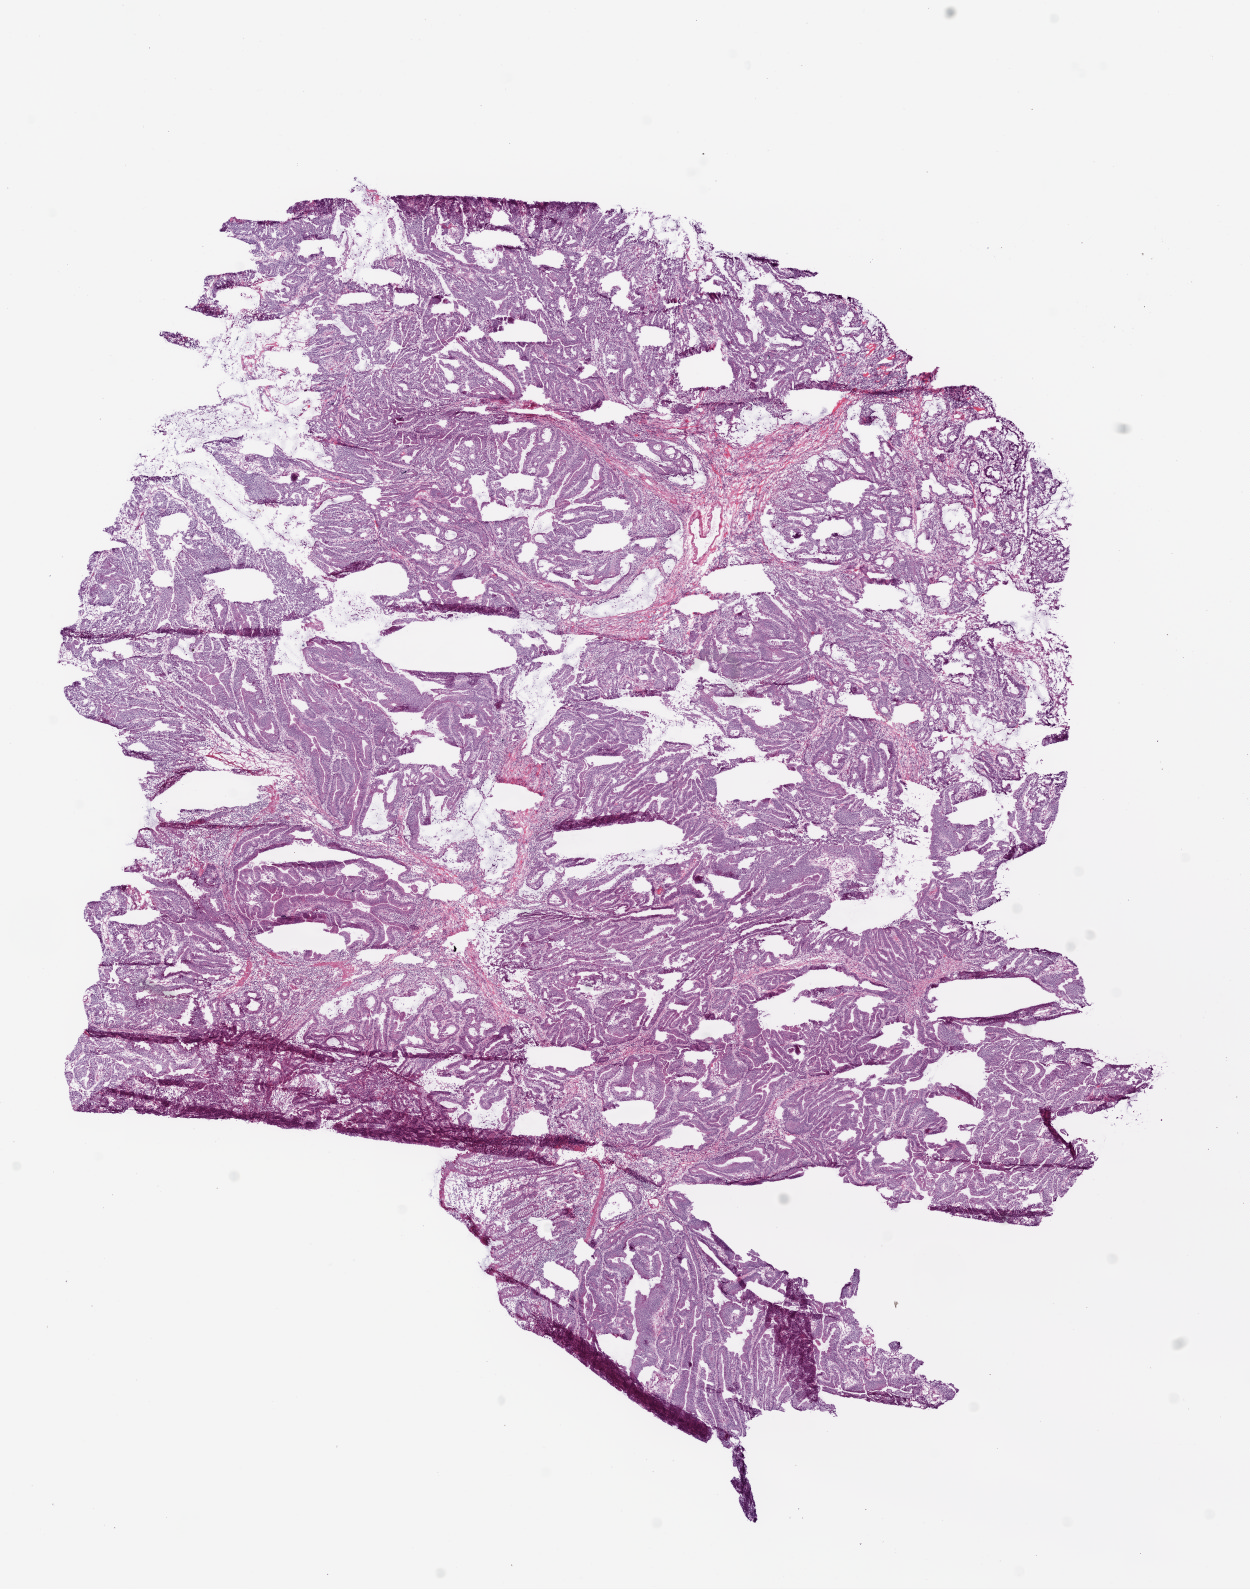
Digitized H&E-stained tissue section (whole slide), a low-resolution overview of the entire scanned area, about 10.0 x 12.8 mm, frozen section, sample: primary tumour, colon. Female patient; age at initial diagnosis 81 years. Composition of this section per pathologist review: tumour cells 90%, tumour nuclei 95%, normal cells 0%, stromal cells 10%, necrosis 0%.
AJCC pathologic stage: IIA (6th edition). Diagnosis: Adenocarcinoma, NOS (cecum).